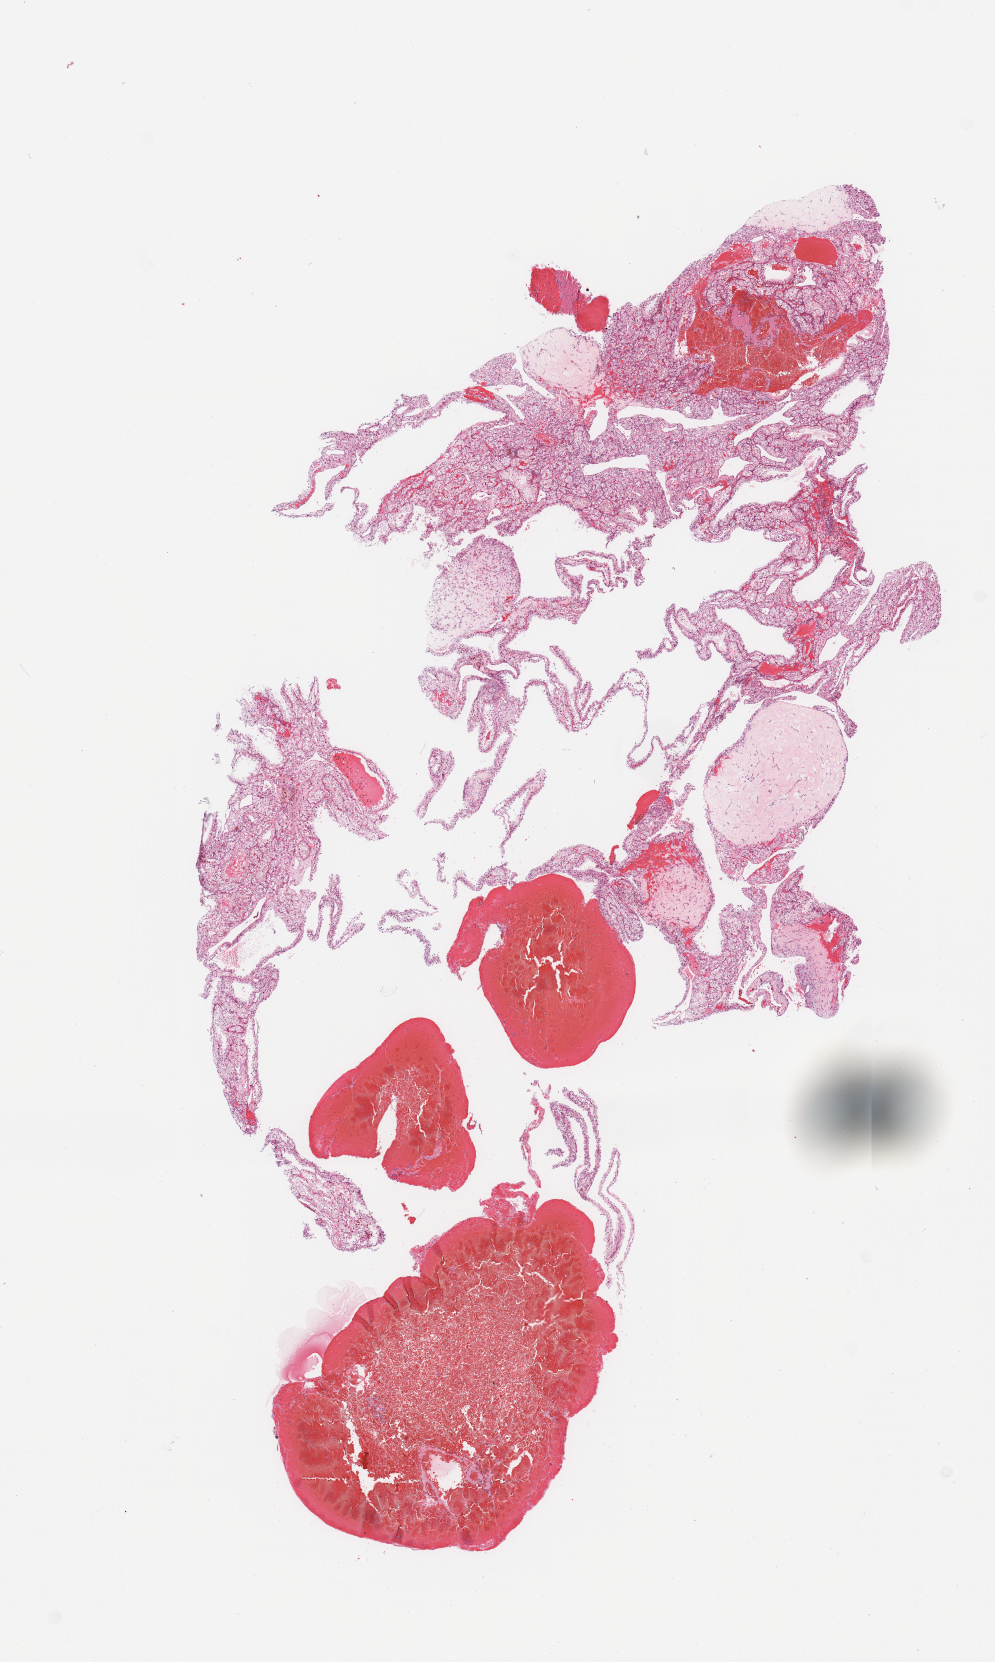
Digitized Hematoxylin and eosin (H&E) stained tissue section (whole slide), low-resolution overview of the scanned area, about 7.9 x 13.2 mm (acquisition: 20x scan), tumour tissue sample, sampled site: kidney. Patient: male, age 57 years.
Histologic diagnosis: Renal cell carcinoma, NOS.